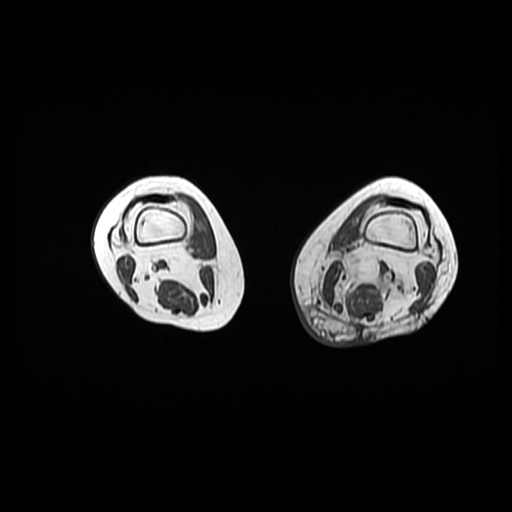
MRI of an extremity soft-tissue mass, one axial slice. Slice 15 of 42 in the series (ordered by position). 6 mm slice thickness. 512 × 512 image matrix, field of view 420 × 420 mm. Female patient. Case-level facts recorded for this patient, not image findings: histological type: pleomorphic leiomyosarcoma; grade: high; site of the primary tumour: left thigh.
Annotated regions visible in this slice (outlined manually by an expert reader):
- gross tumour volume including surrounding oedema: box from (x=317, y=257) to (x=392, y=315) px